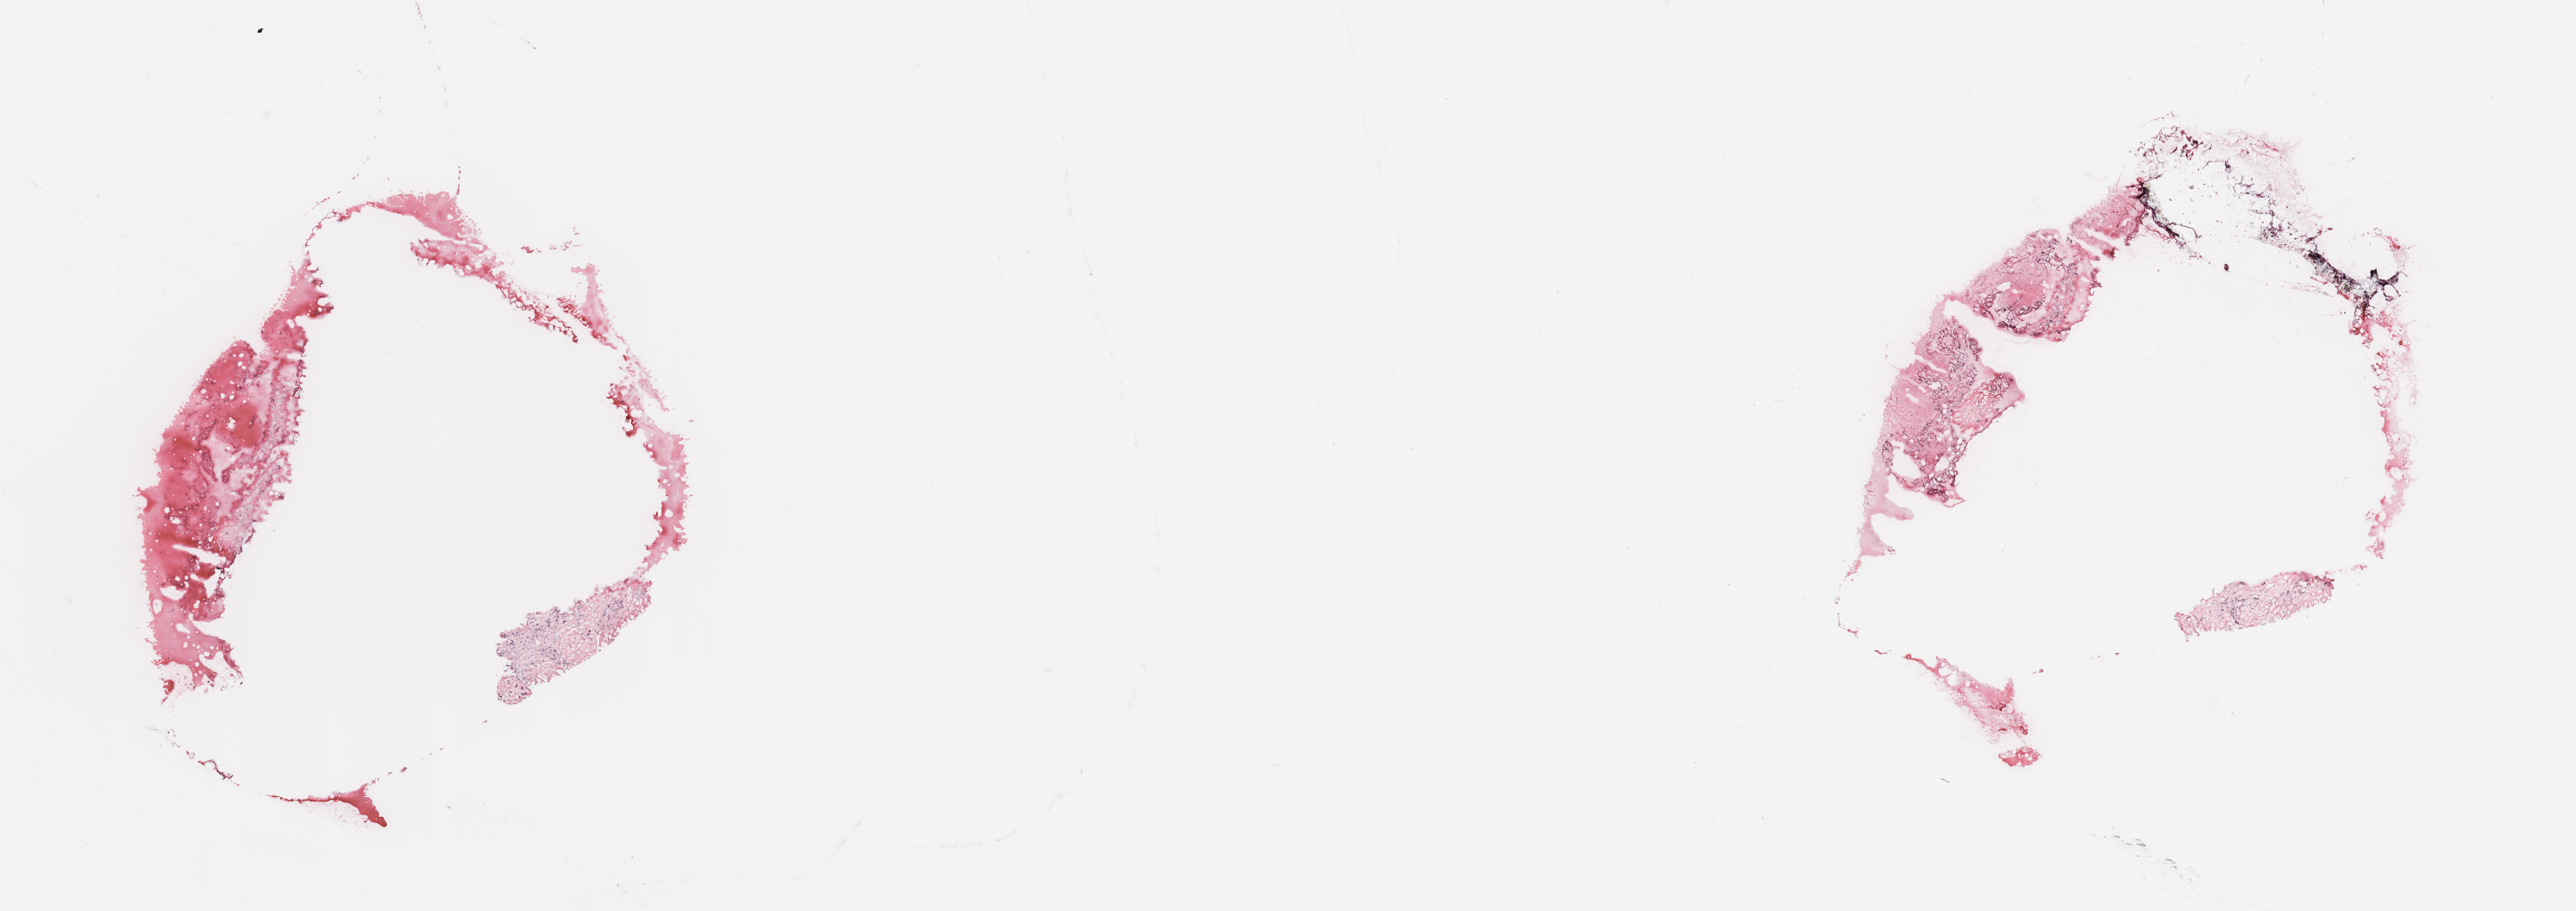
H&E-stained whole-slide image, shown as a low-resolution overview of the whole scanned area (about 23.6 x 8.4 mm); breast, tissue type not recorded.
* patient diagnosis (cohort enrolment): breast cancer (breast)